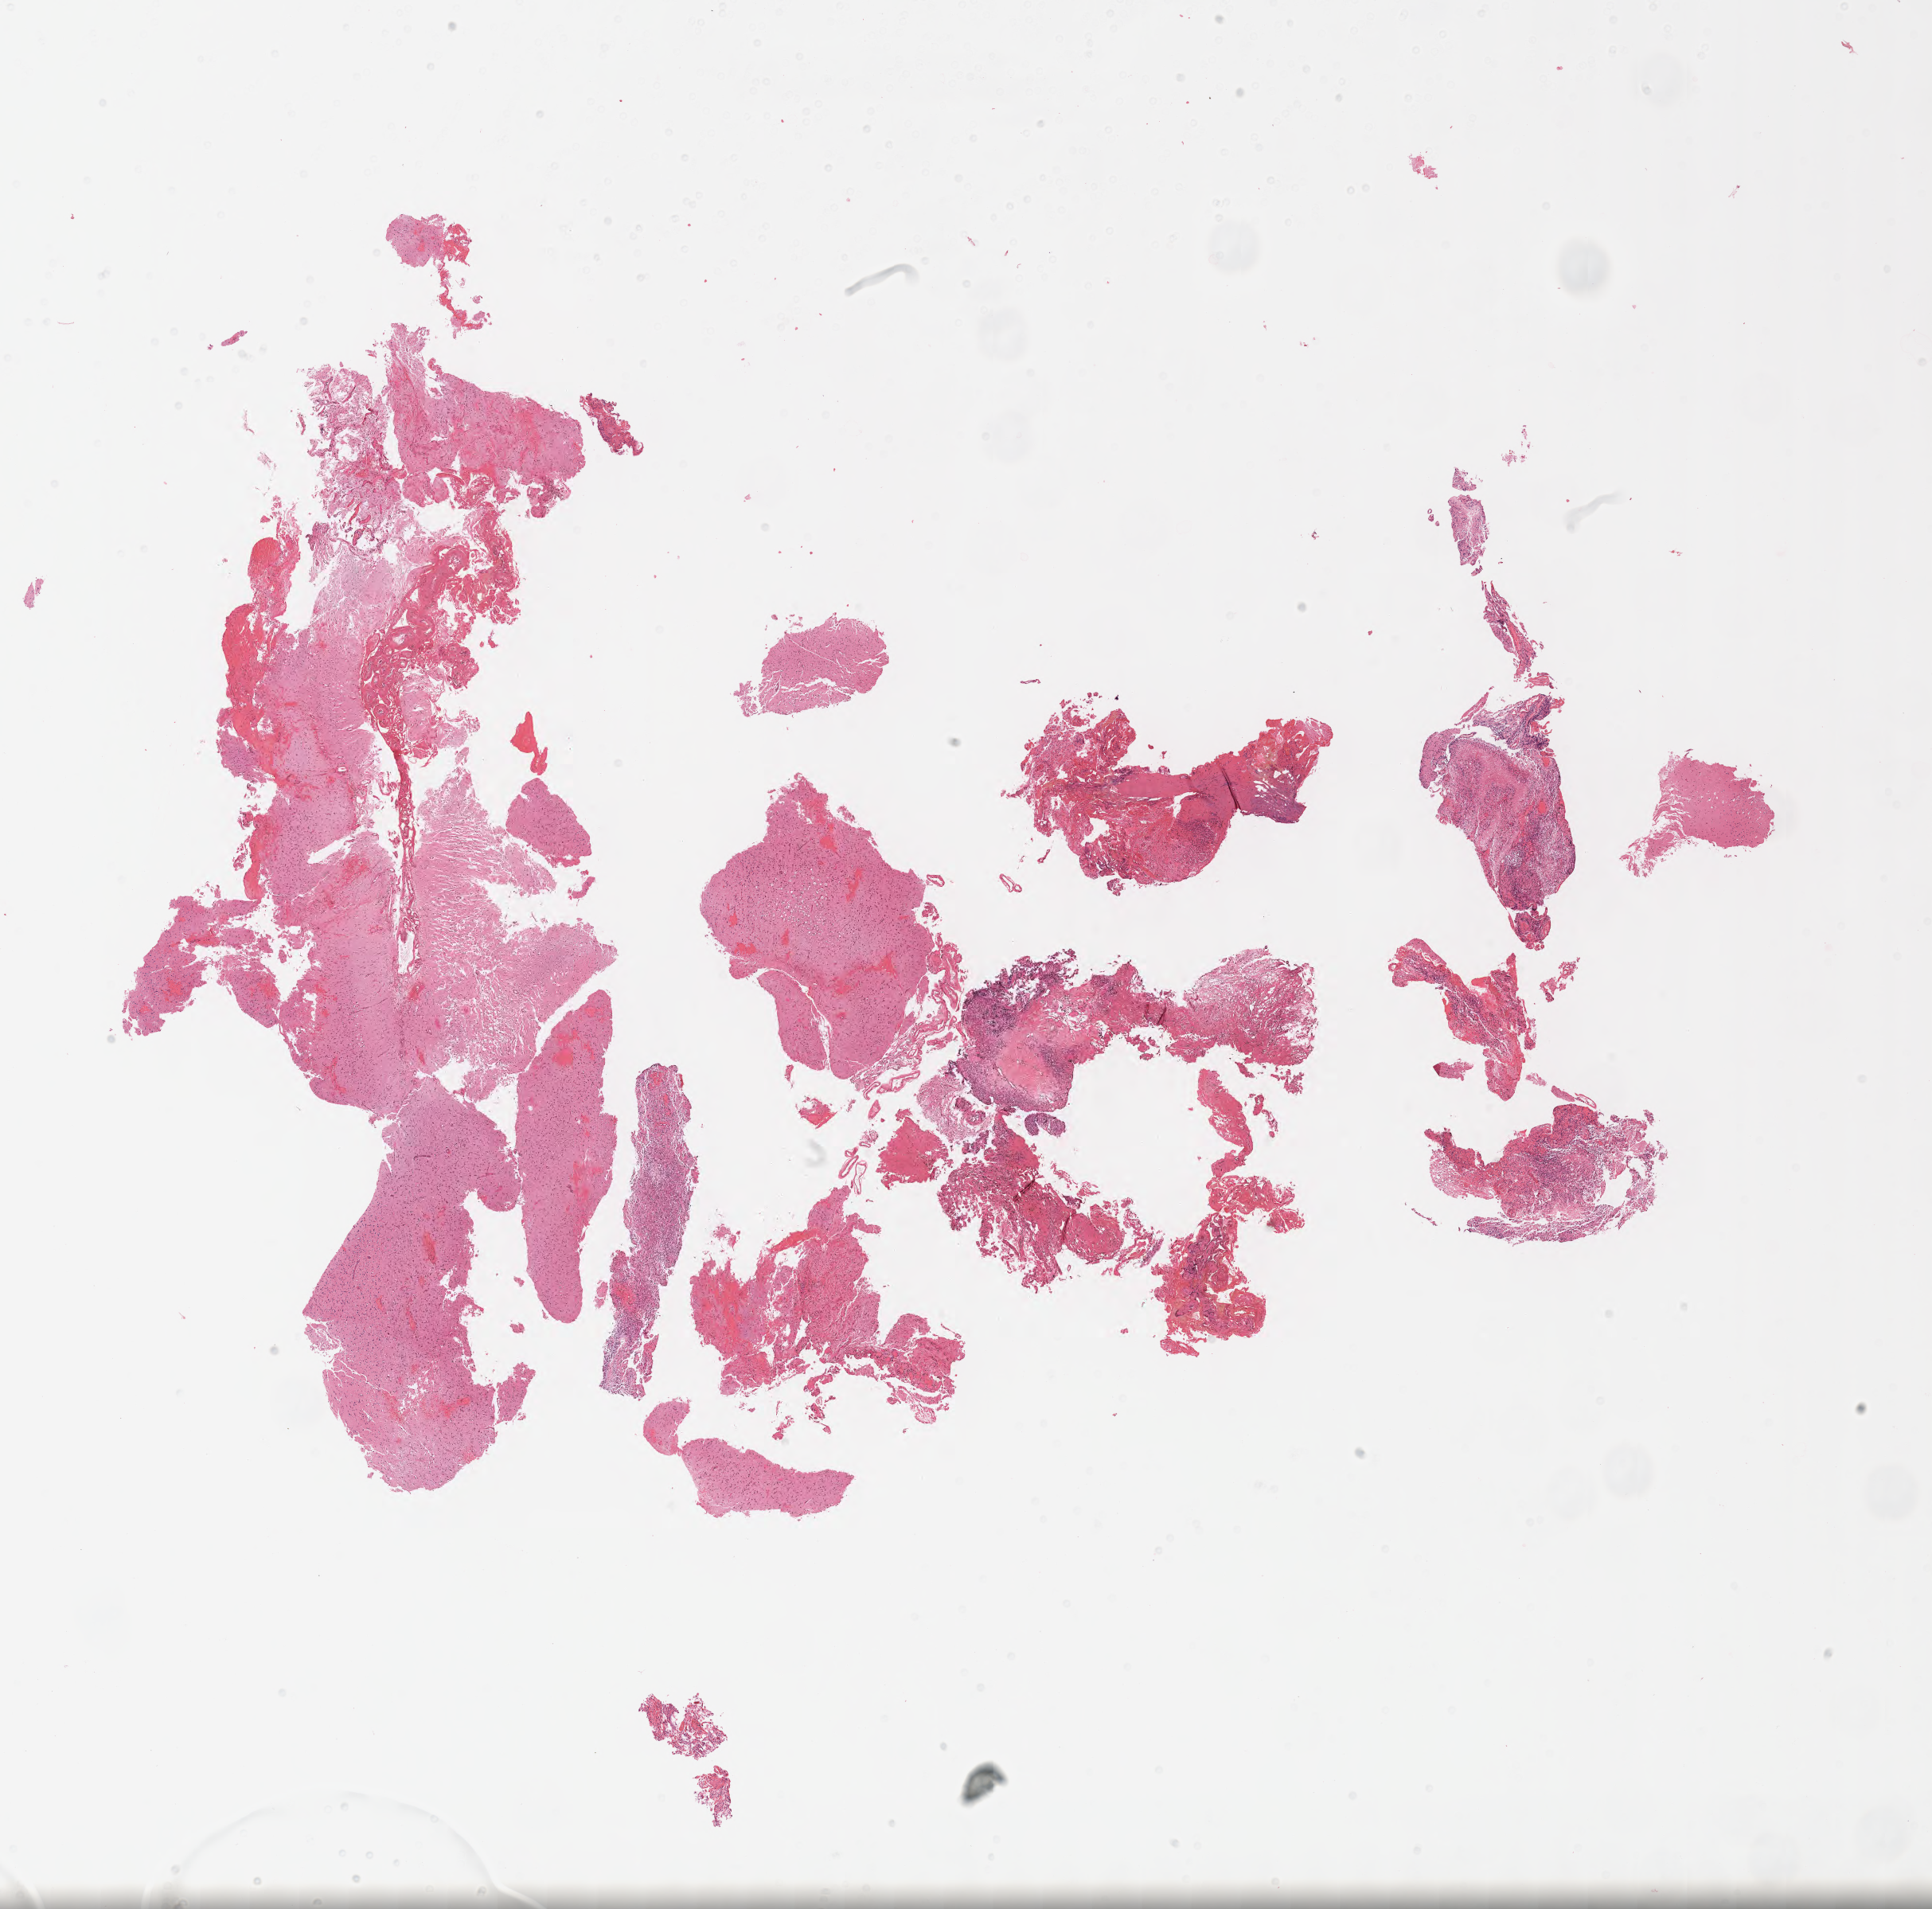
Digitized H&E-stained section, shown as a low-resolution overview of the whole scanned area (about 19.6 x 19.4 mm), FFPE section, specimen: recurrent tumor, site: brain. Male patient; age at initial diagnosis 59 years. Composition of this section per pathologist review: tumor cells 35%, tumor nuclei 53%, stromal cells 31%, necrosis 3%, normal cells 31%. Inflammatory infiltration, as recorded: lymphocyte infiltration 0%, monocyte infiltration 0%, neutrophil infiltration 0%.
• patient diagnosis: Glioblastoma, NOS